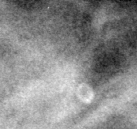
Region of interest cut from a scanned film mammogram (one marked finding); left breast; MLO view.
Marked abnormality: calcifications, morphology lucent center / punctate; BI-RADS assessment category 2; benign without callback (not worked up further).